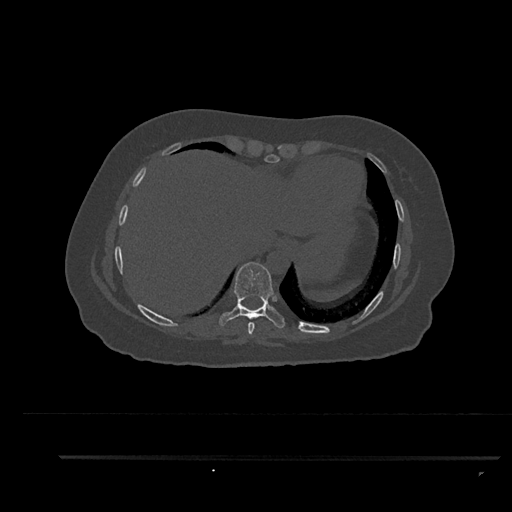
CT including the spine, one axial slice; slice 420 of 797 in the series (ordered by position); reconstruction kernel Br40s/3; bone window (W 1800 / L 400 HU); 0.5 mm slice thickness; 512 × 512 image matrix, field of view 408 × 408 mm. Patient: female, 44 years. Case-level facts recorded for this patient, not image findings: primary cancer: renal.
Outlined on this slice (semi-automatically segmented with operator editing):
- T8 vertebra: bounding box [x1, y1, x2, y2] px = [248, 322, 255, 335]
- T9 vertebra: [219, 262, 285, 328]